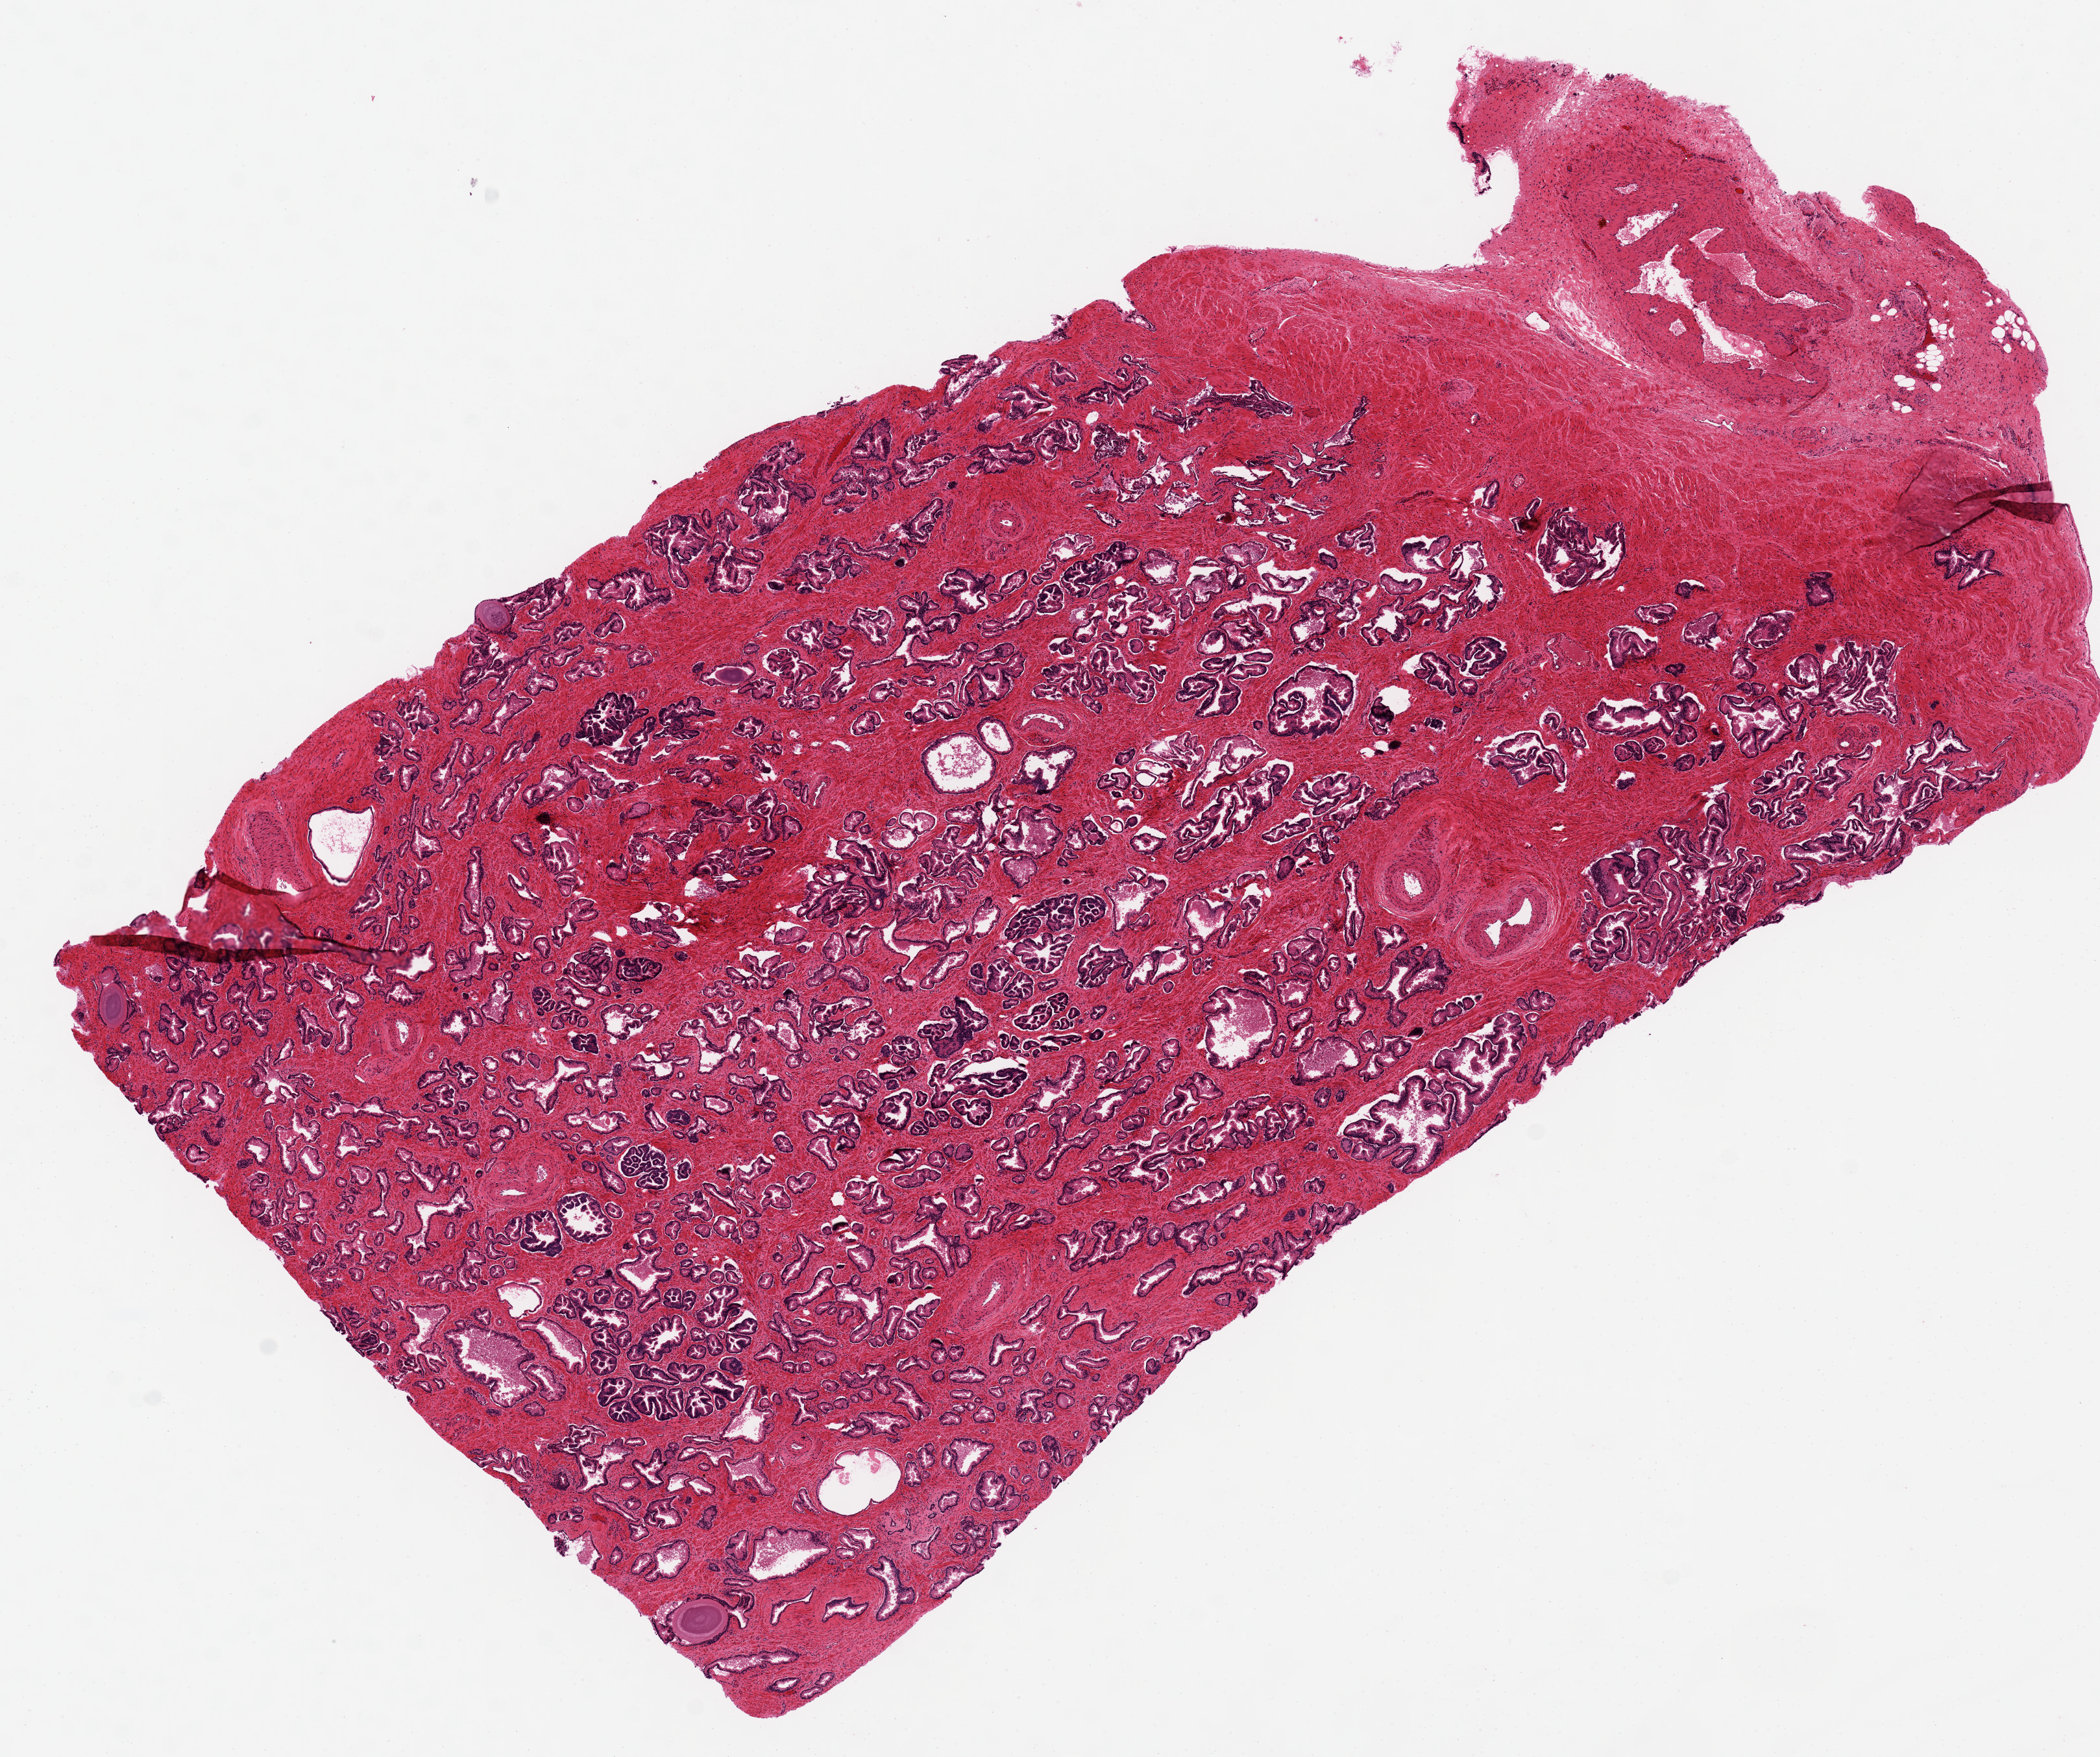
Whole-slide image, hematoxylin and eosin (H&E) stain, brightfield — shown as a low-resolution overview of the whole scanned area (about 12.8 x 10.7 mm); PAXgene-fixed, paraffin-embedded tissue; target tissue: prostate; donor tissue sample. Donor: male.
Reviewer comment on this tissue sample: Glands remarkably well-preserved.